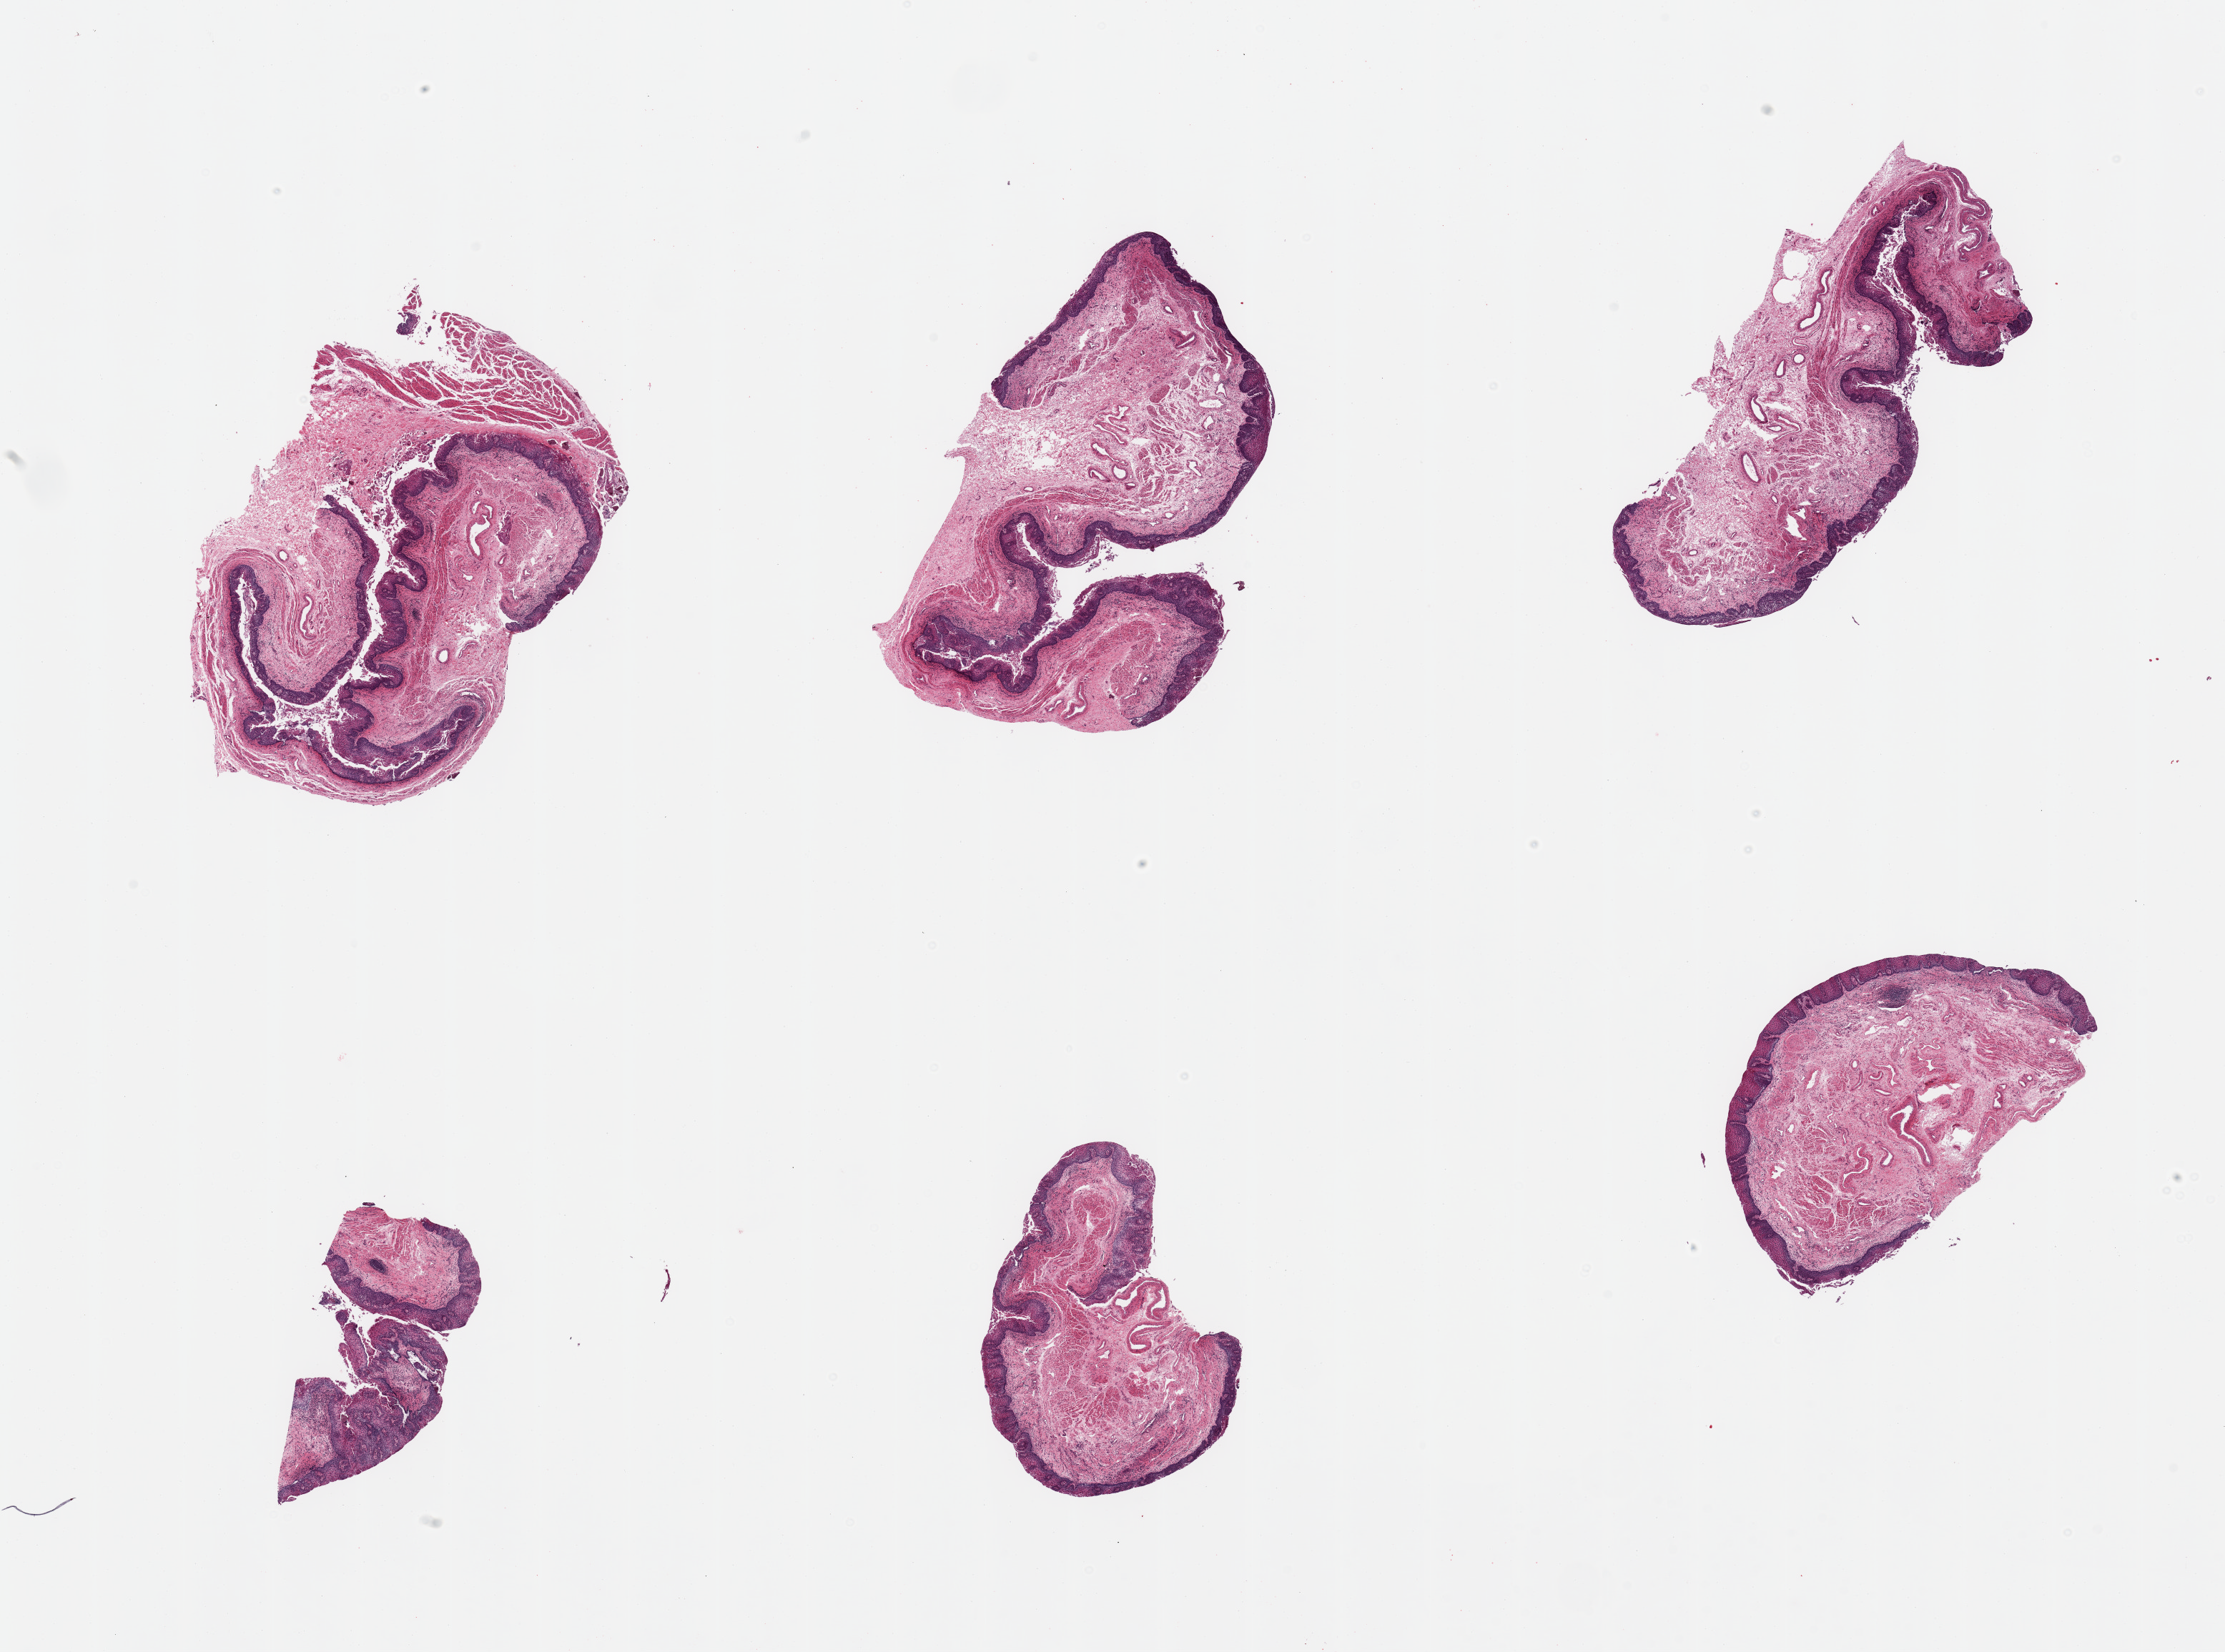
Digitized H&E-stained section, shown as a low-resolution overview of the whole scanned area (about 24.6 x 18.3 mm), PAXgene-fixed, paraffin-embedded tissue, sampled site (target tissue): esophageal mucous membrane, tissue donor sample. Donor: male.
Pathologist's review note for this sample: 6 pieces; superficial epithelial desquamation; squamous epithelium ~0.3mm thick, esophagitis, small portion of muscularis.